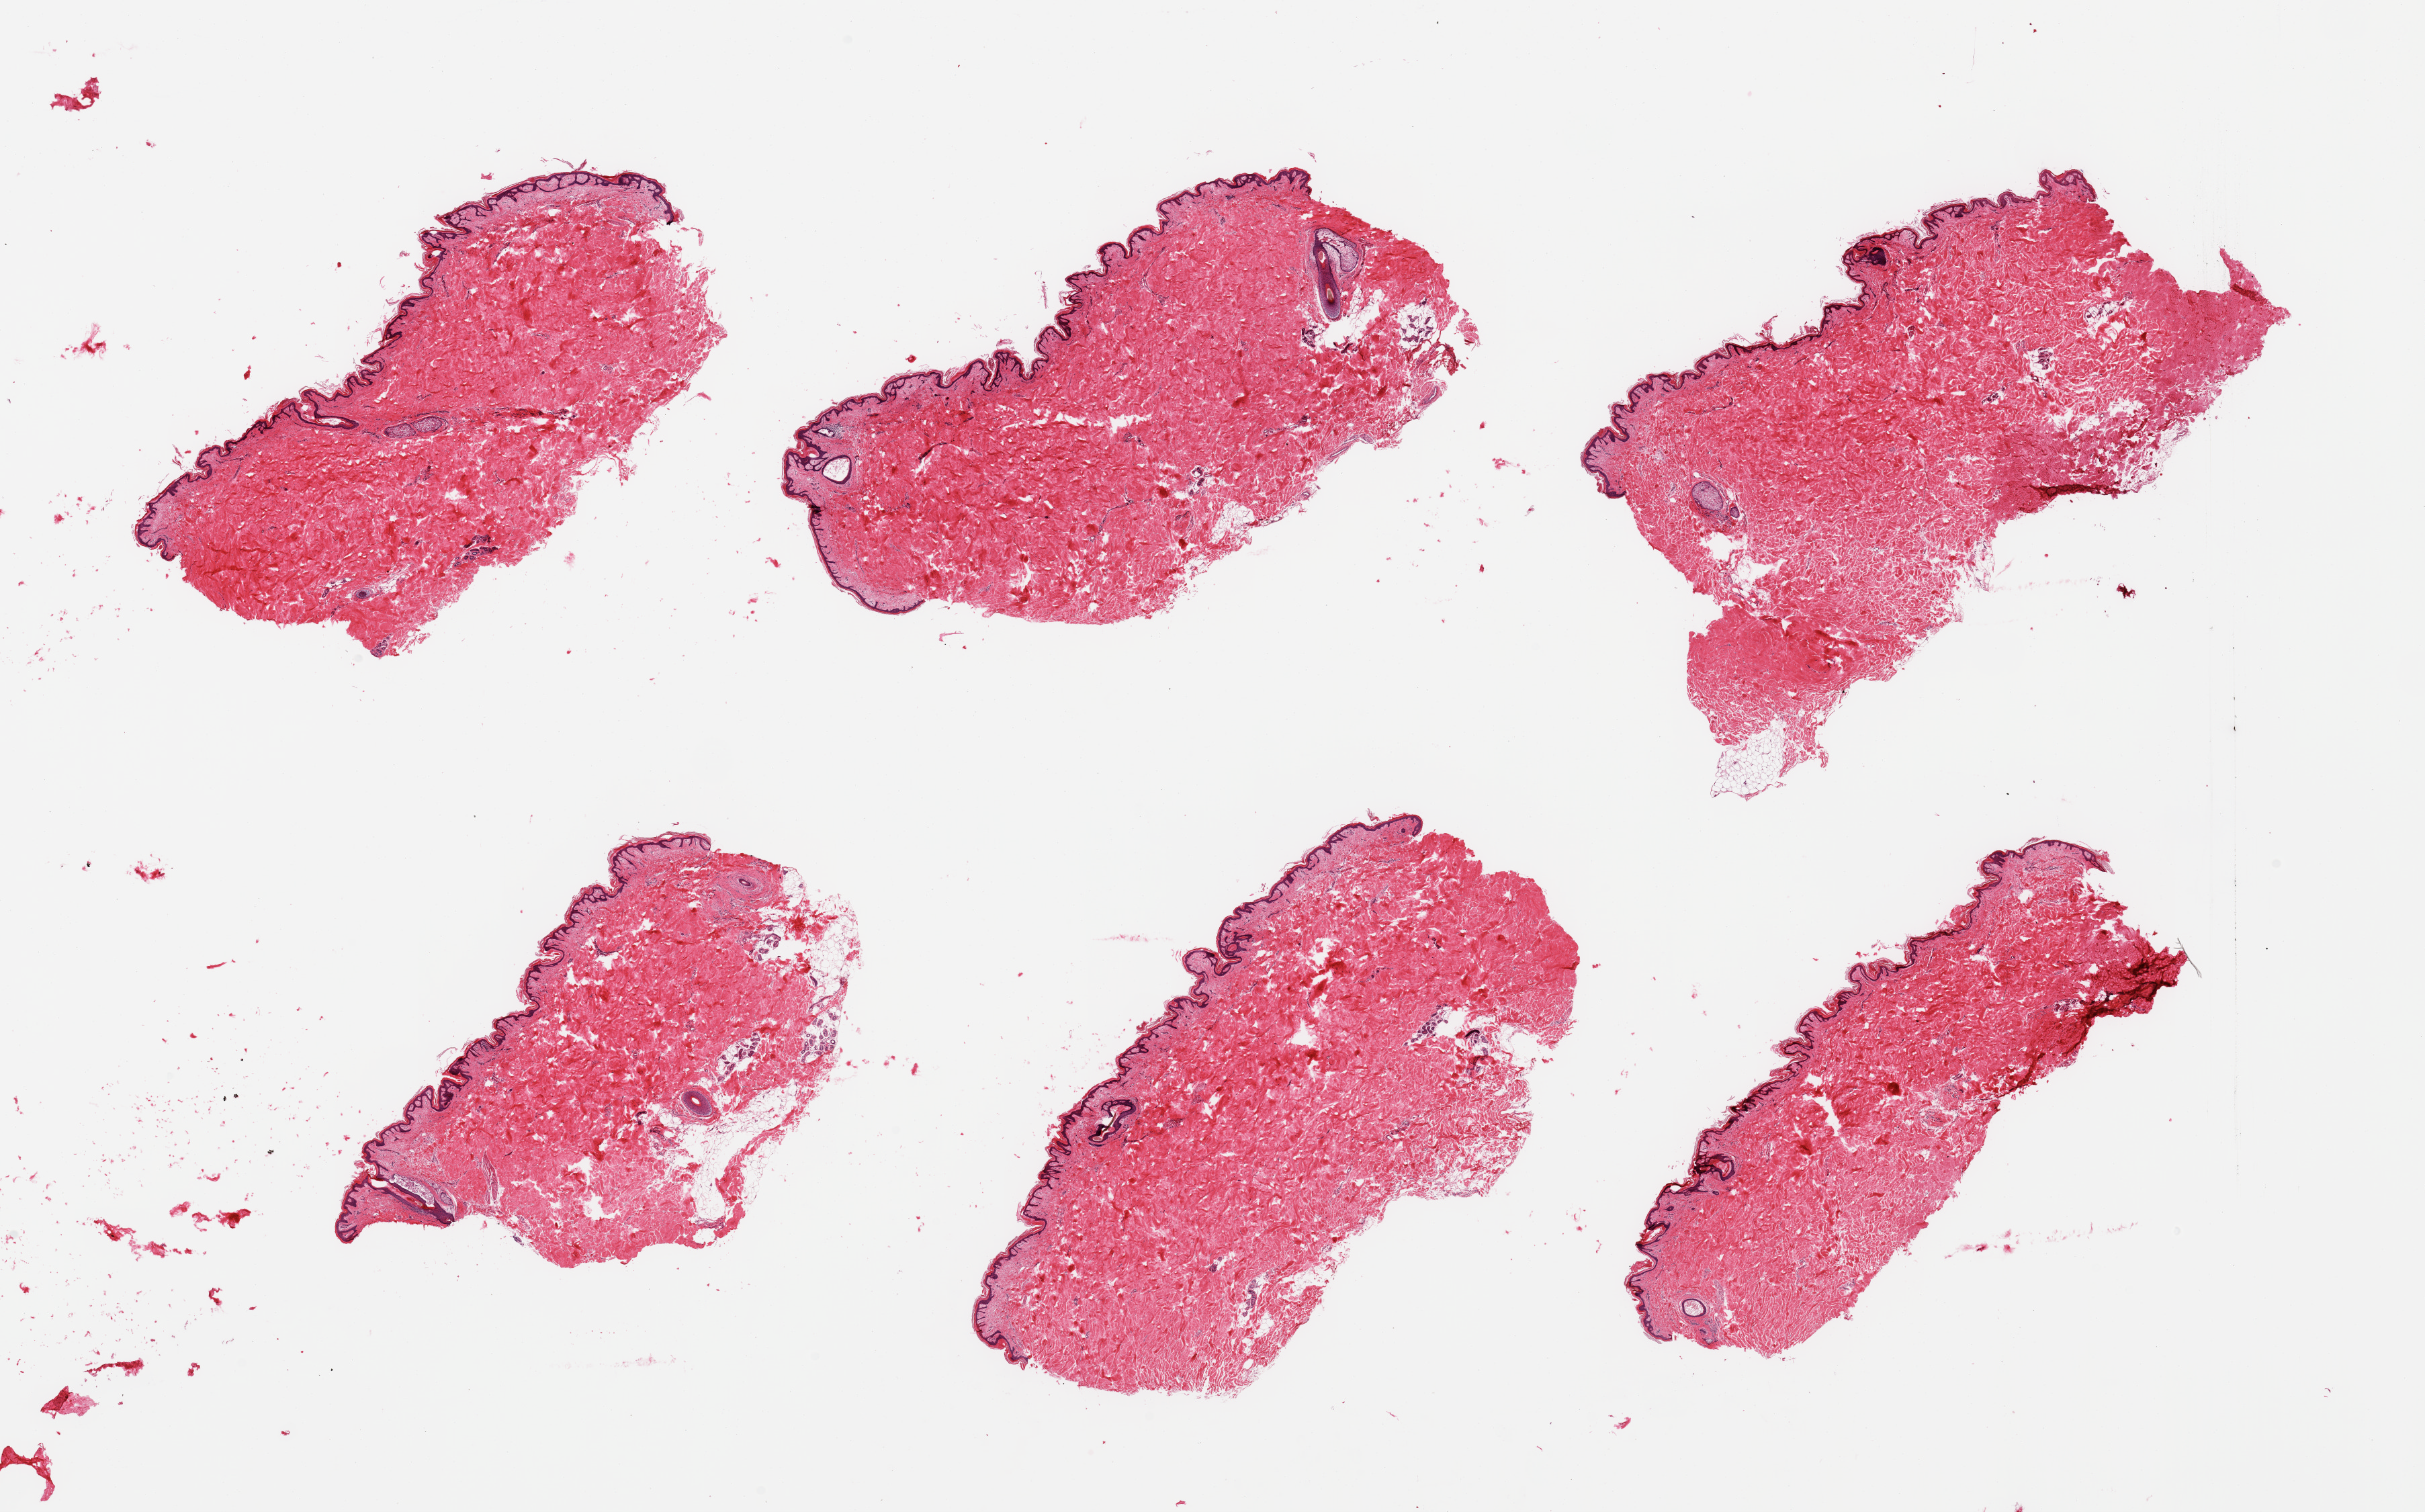
H&E whole-slide image — whole scanned area (about 28.5 x 17.8 mm, from a 20x scan) shown as a low-resolution overview. PAXgene-fixed, paraffin-embedded tissue. Sampled site (target tissue): skin of suprapubic region. Tissue donor sample. Male donor.
Review note (as recorded): 6 pieces; keratosis.